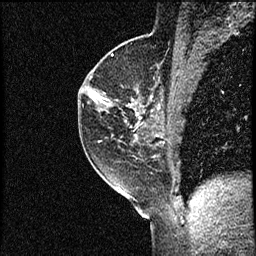
Breast MRI (dynamic contrast-enhanced), one sagittal slice; slice 38 of 56 in the series (ordered by position); dynamic contrast-enhanced study with each time point stored as its own series, time point 2 of 3 at this slice position (early post-contrast, ordered by acquisition time); 1.5 T; TE 4.2 ms, TR 17.3 ms; 2 mm slice thickness; 256 × 256 image matrix, field of view 200 × 200 mm. Female patient. From the clinical record (not read from this slice): setting: breast cancer imaged before/during neoadjuvant chemotherapy; receptor status: HER2-positive.
Outlined on this slice (semi-automatically segmented with operator editing):
- analysis volume of interest (the breast-tissue region the enhancement analysis was run in; not a lesion): bounding box <77,50,156,155> (left, top, right, bottom; pixels)
- tumour enhancement mask (voxels above the 100 % enhancement threshold inside the analysis volume of interest): <90,92,141,119>